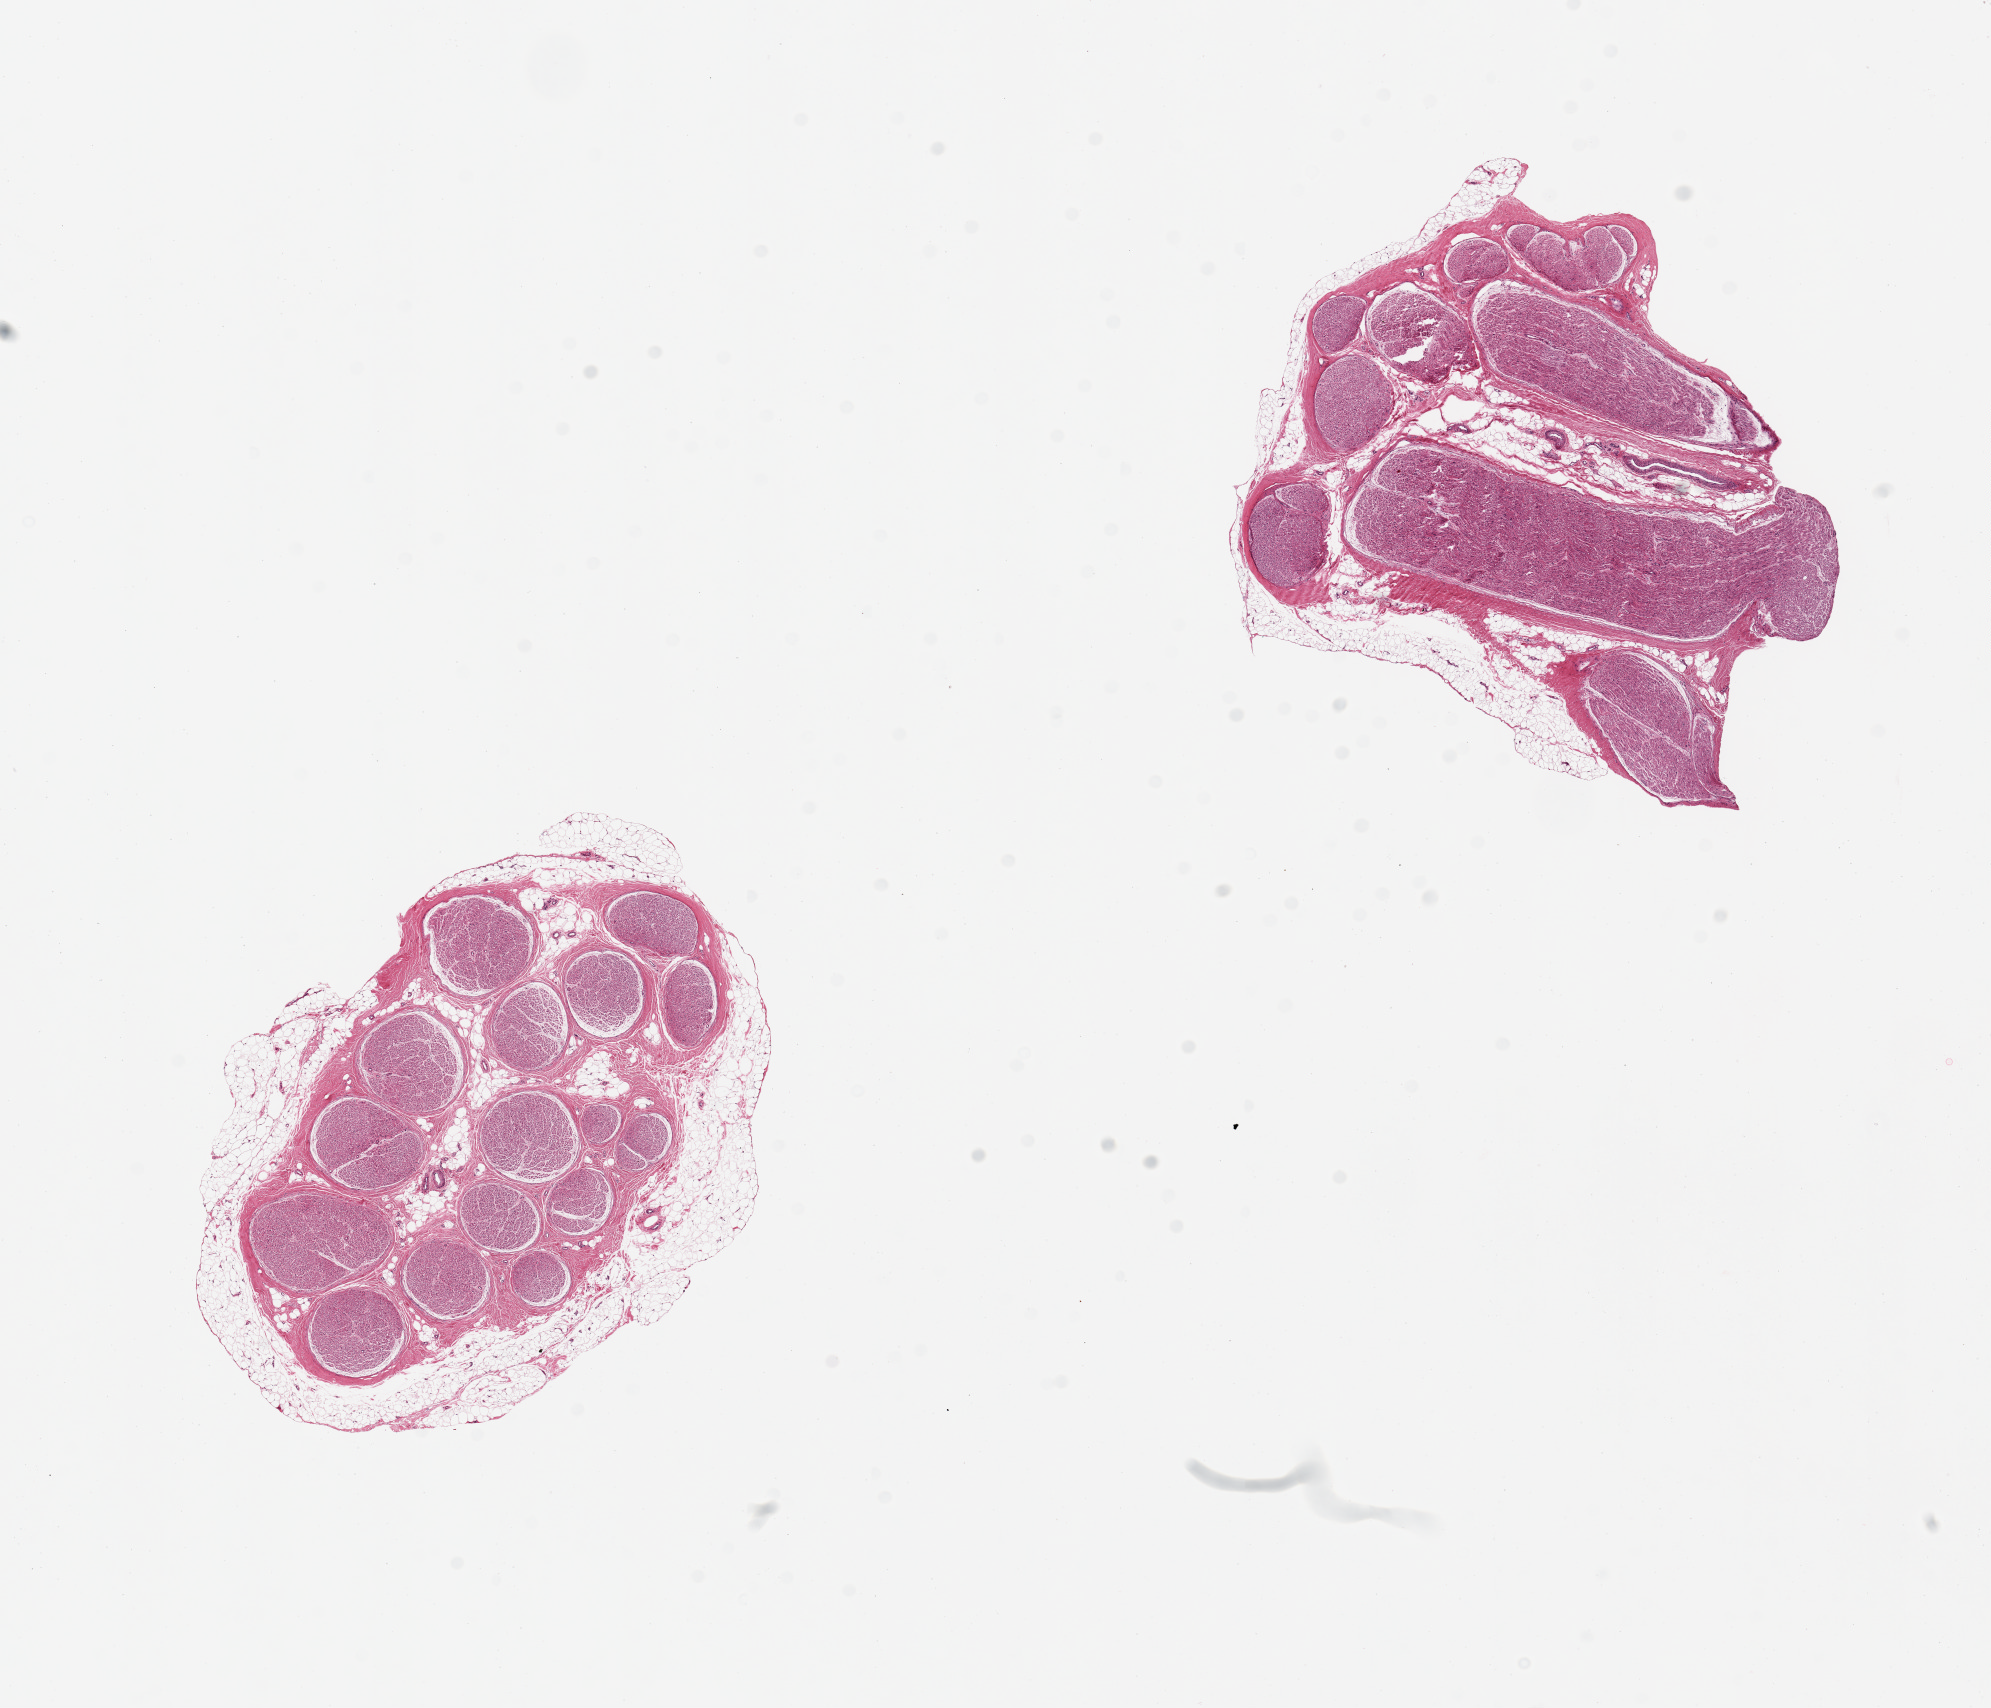
Digitized hematoxylin and eosin (H&E)-stained section — a low-resolution overview of the entire scanned area, about 15.8 x 13.5 mm (acquisition: 20x scan). PAXgene-fixed paraffin-embedded (PFPE) section. Sampled site (target tissue): tibial nerve. Donor tissue sample. Donor sex: female.
Review note (as recorded): 2 pieces, 5.5x4 & 5x4.5mm; discontinous rim of adherent fat up to ~0.7mm on one.